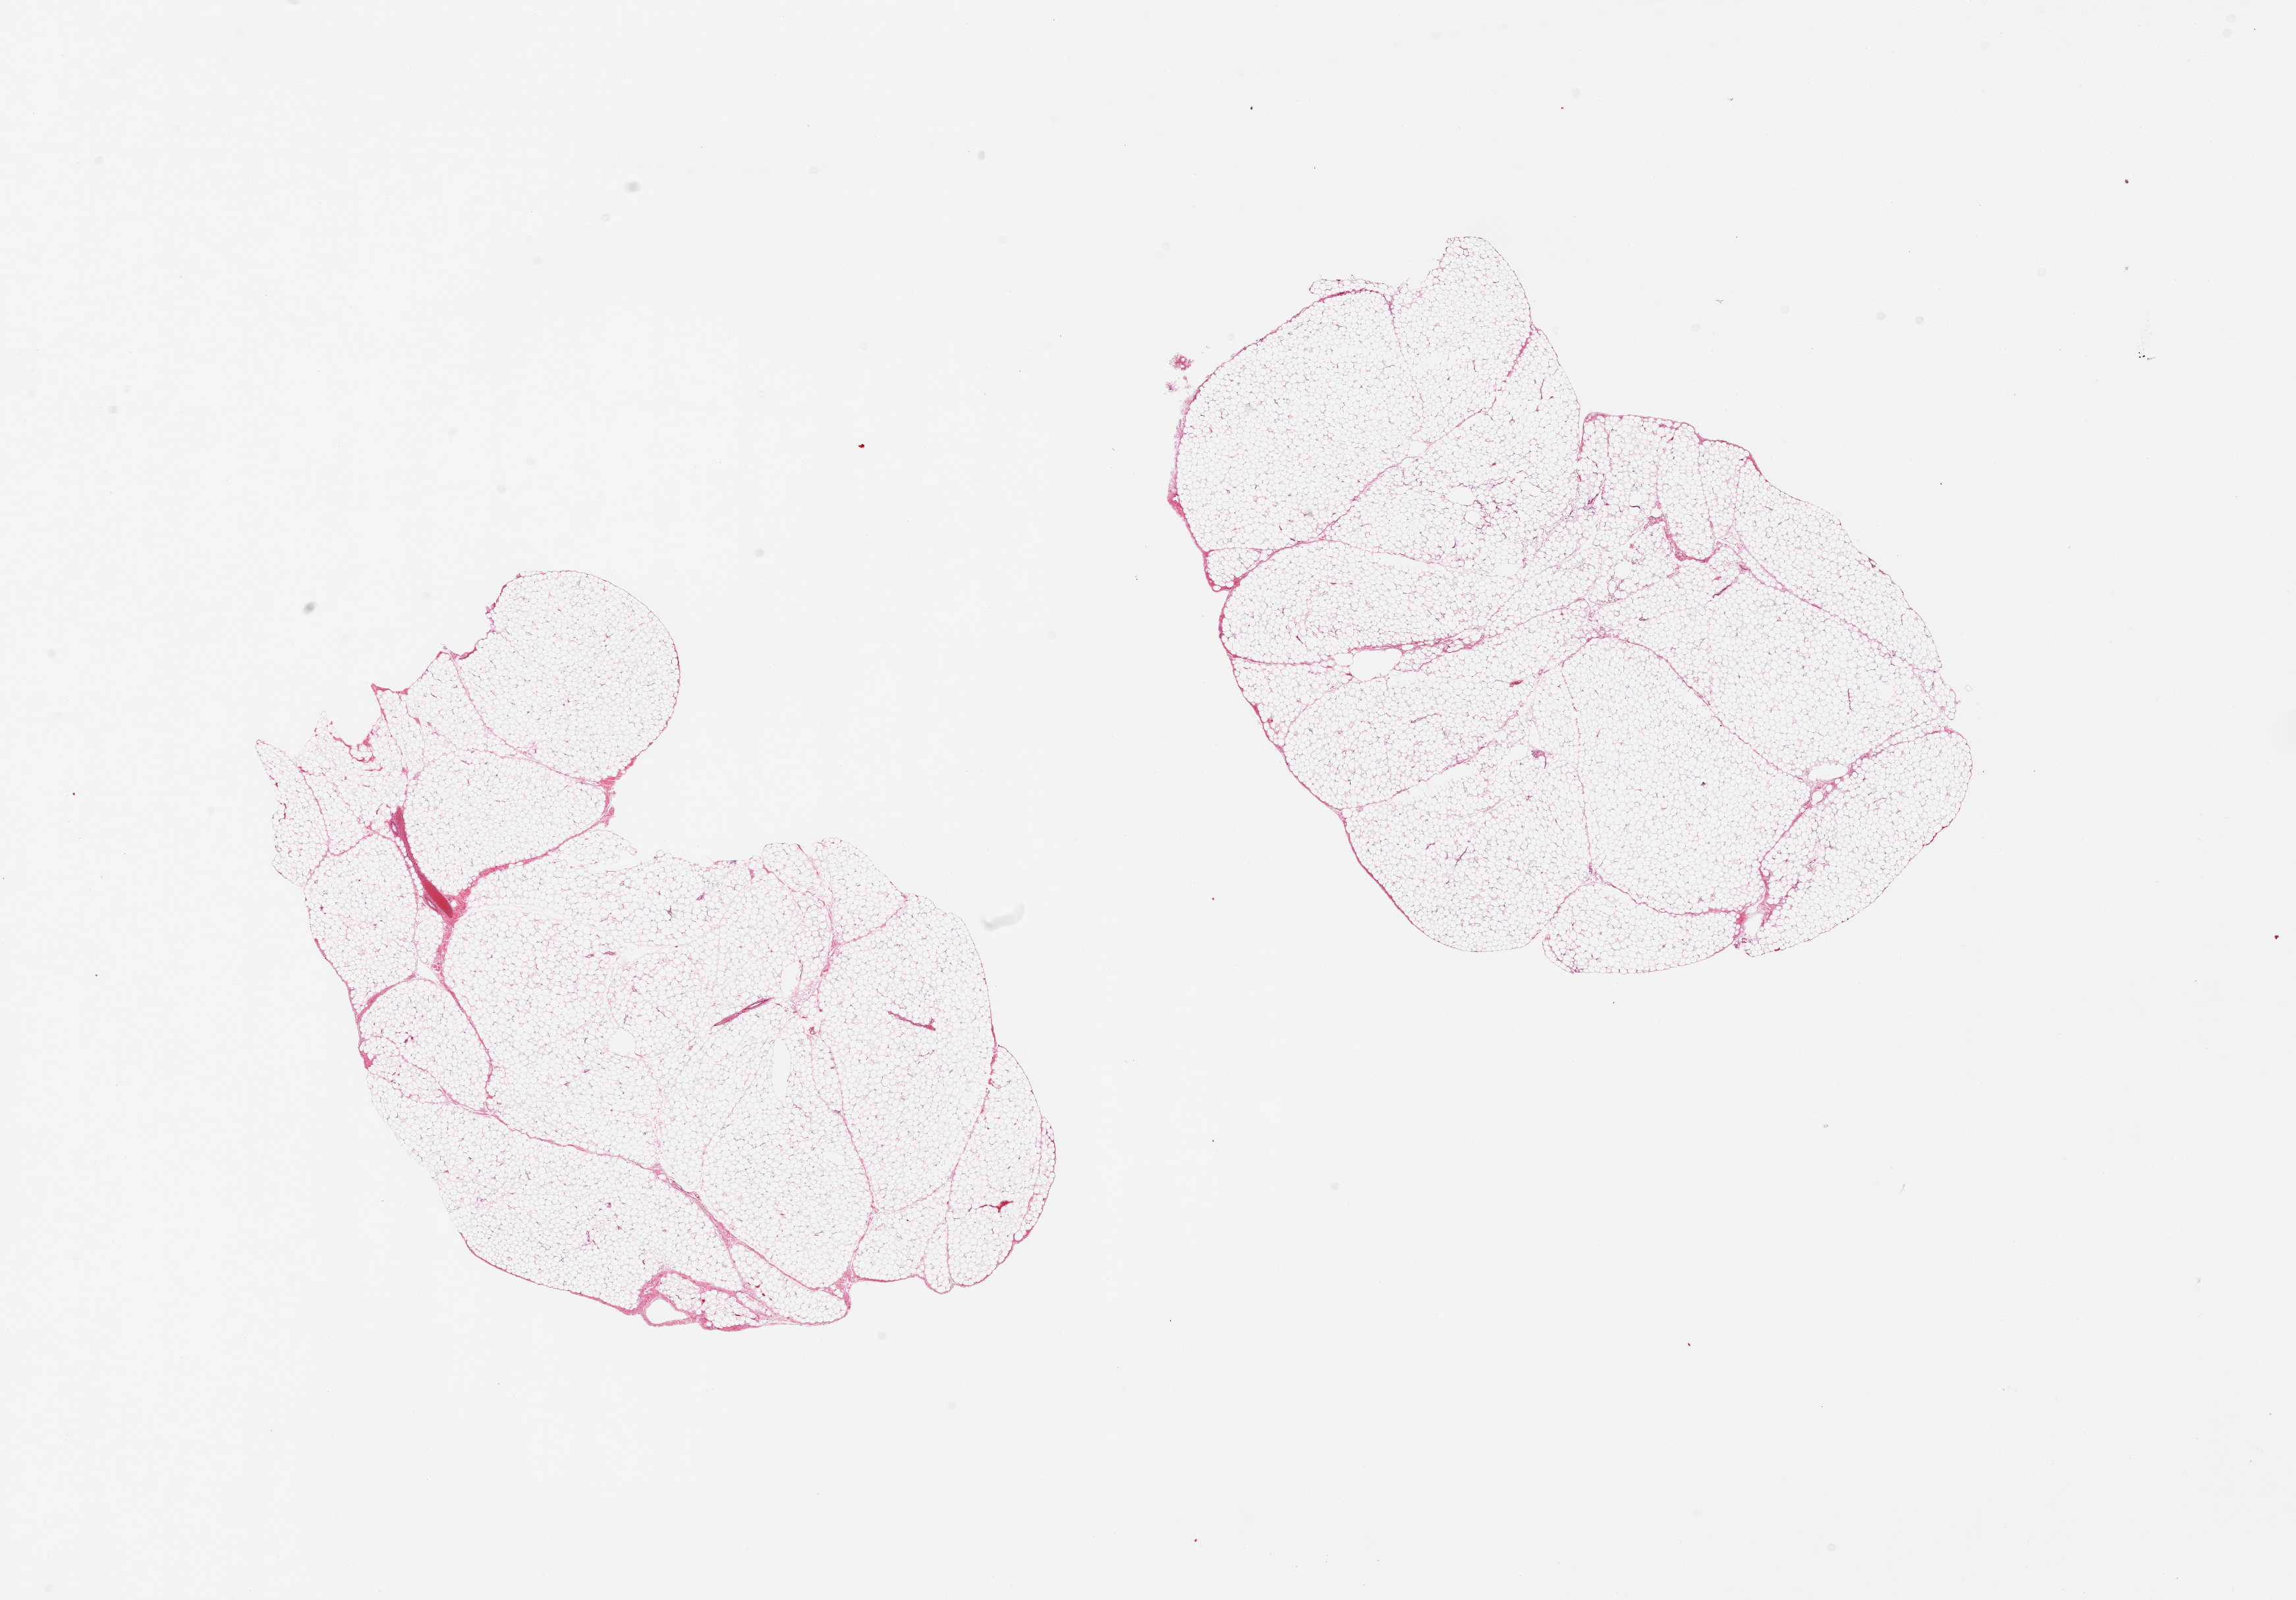
Digitized haematoxylin and eosin-stained section — whole scanned area (about 27.6 x 19.2 mm) shown as a low-resolution overview; PAXgene-fixed paraffin-embedded (PFPE) section; sampled site (target tissue): omentum; tissue donor sample. Male donor.
• pathologist's review note for this sample: 2 pieces, minimal fibrous/vascular tissue, good specimens